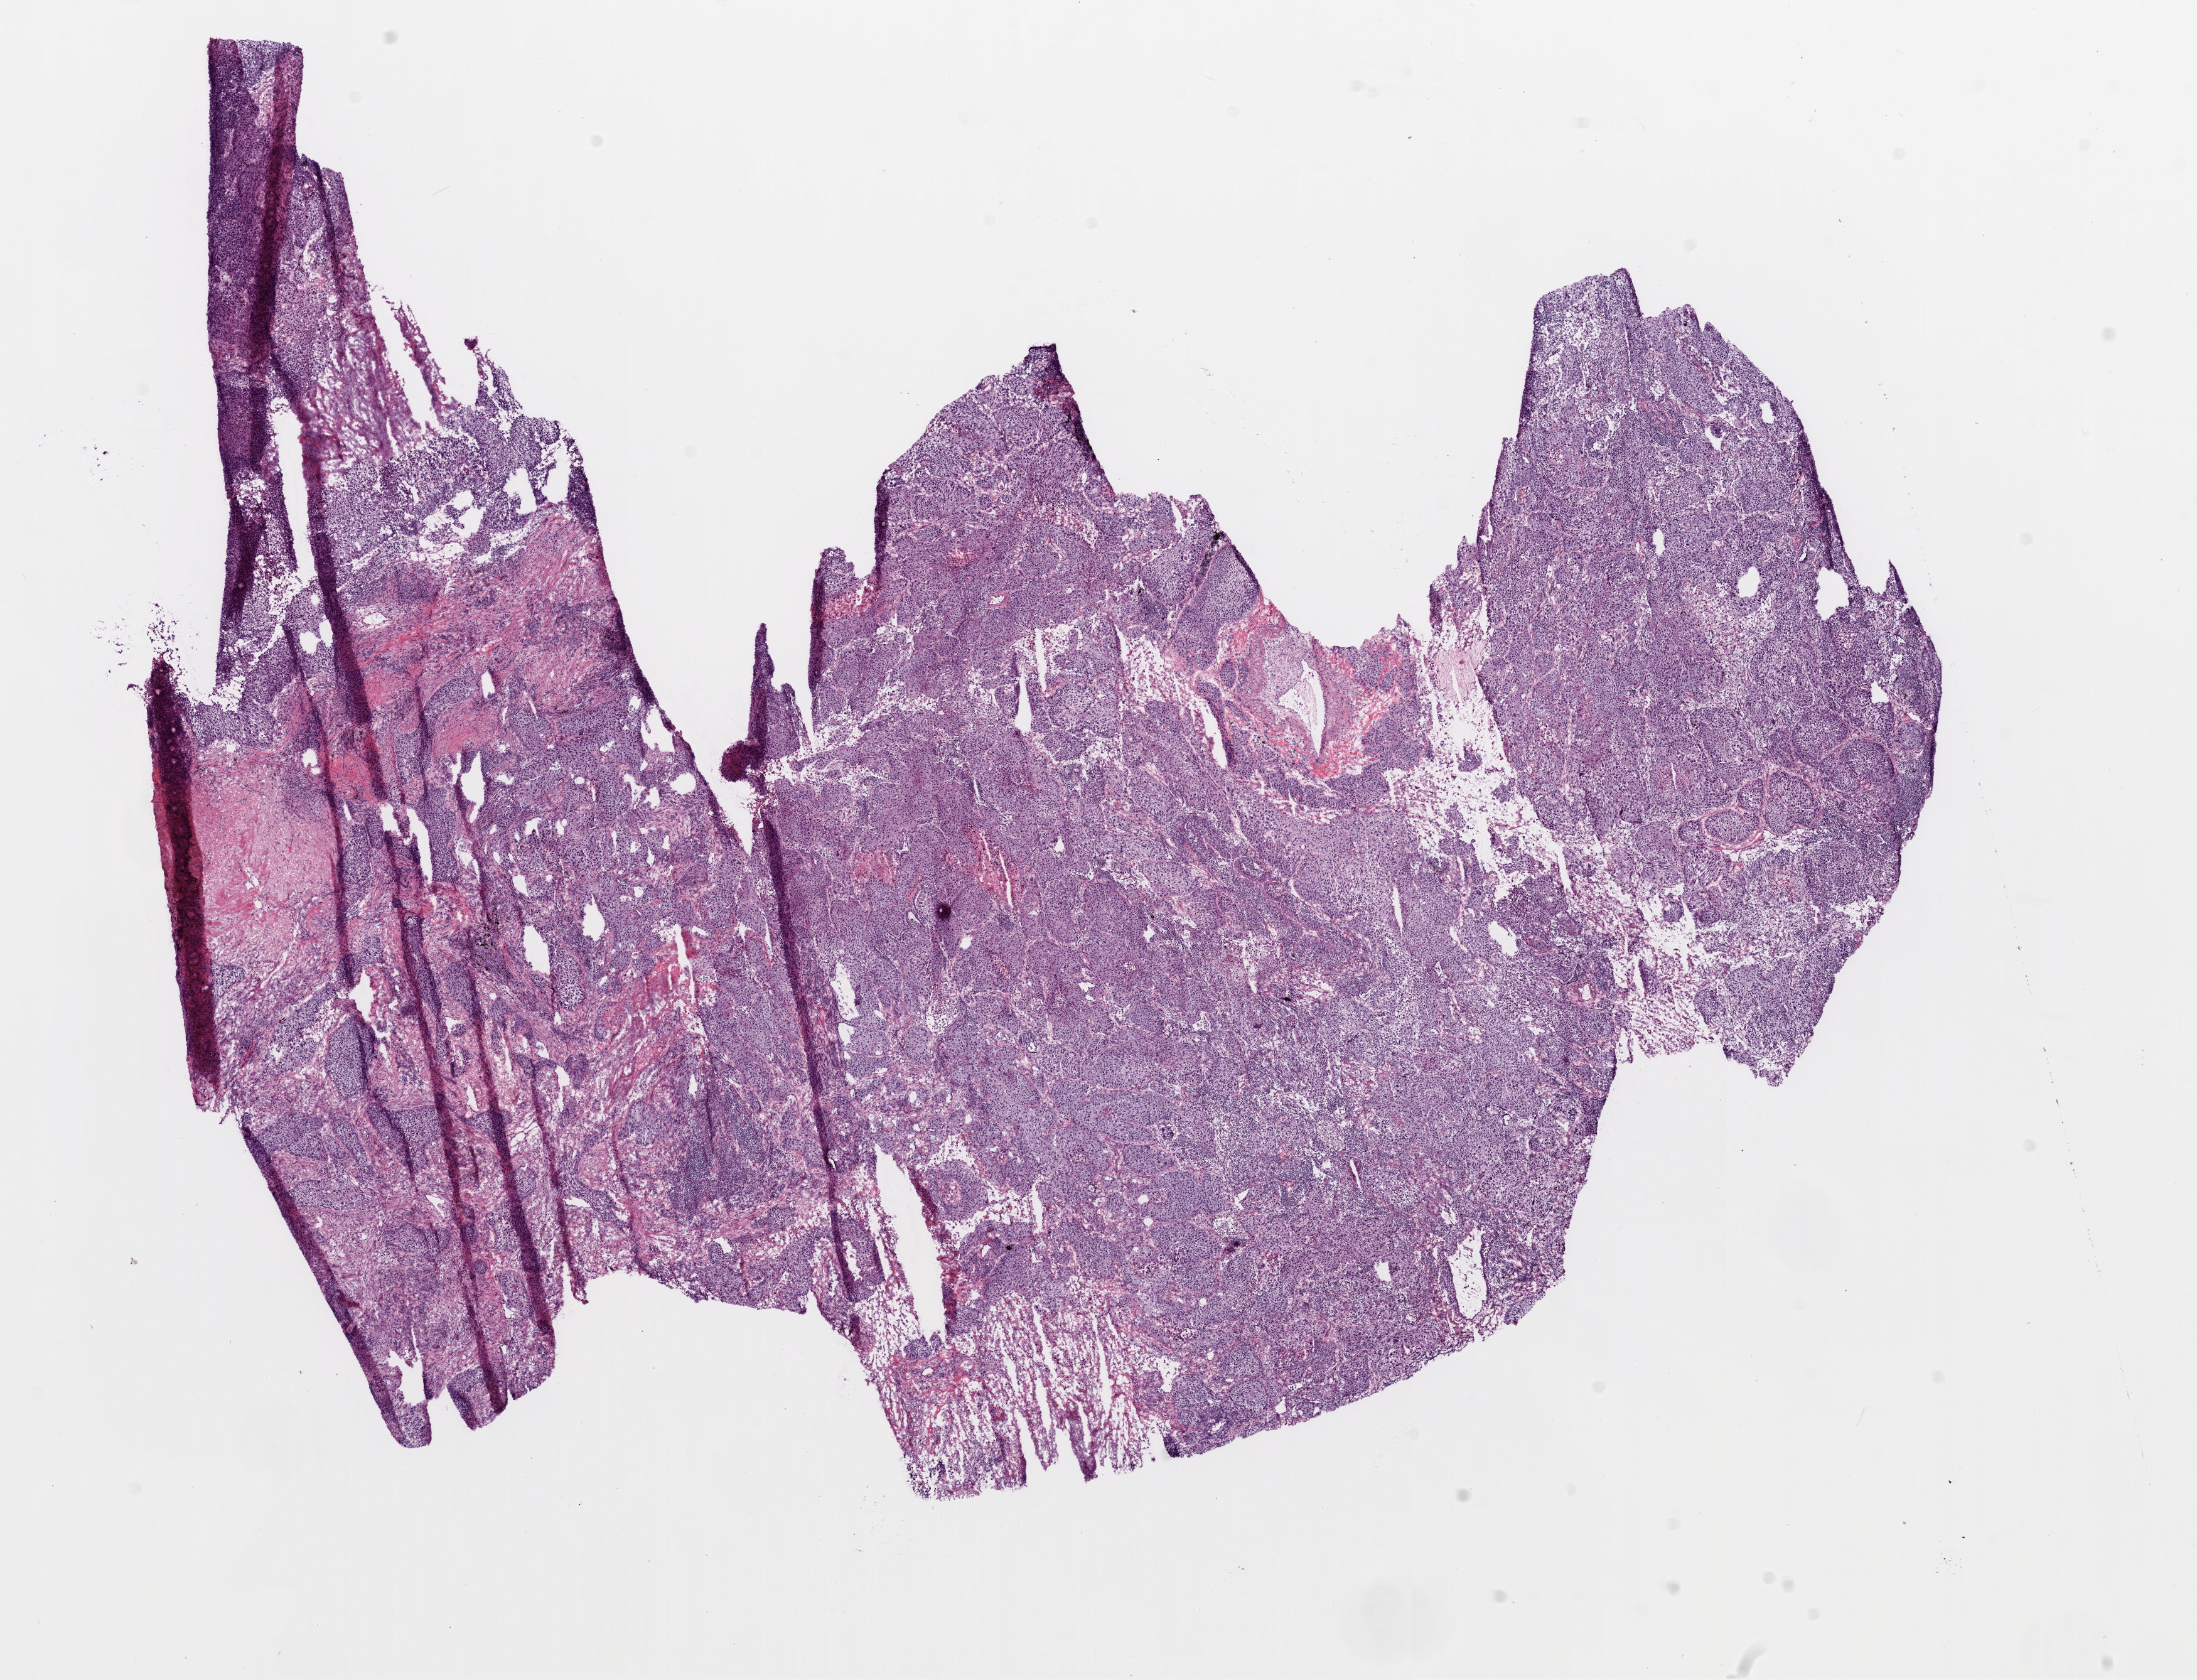
Digitized H&E-stained tissue section (whole slide), a low-resolution overview of the entire scanned area, about 14.0 x 10.7 mm (from a 20x scan), frozen section from the bottom of the tissue portion, primary tumour sample from the lung. Female patient; age at initial diagnosis 63 years. Pathologist review of this section (percent, as recorded): tumour cells 87%, tumour nuclei 85%, normal cells 0%, stromal cells 5%, necrosis 8%.
Diagnosis: Squamous cell carcinoma, NOS. AJCC pathologic stage: IB.